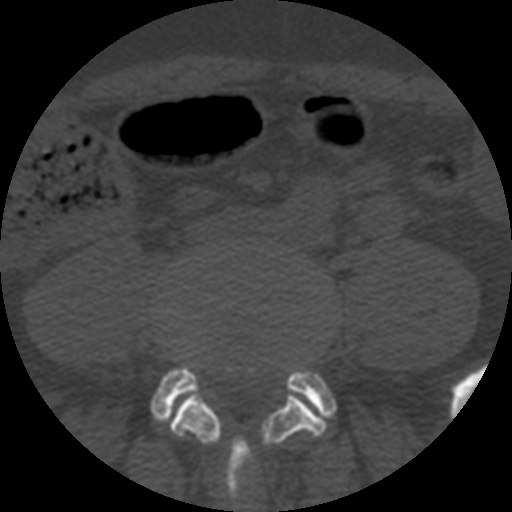
CT including the spine, one axial slice. Position 78 of 508 along the scan axis. Reconstruction kernel STANDARD. Bone window (W 1800 / L 400 HU). 1.25 mm slice thickness. 512 × 512 image matrix. Patient age 57 years. From the clinical record (not read from this slice): primary cancer: prostate.
Annotated regions visible in this slice (semi-automatically segmented with operator editing):
- L4 vertebra: bounding box <170,389,326,509> (left, top, right, bottom; pixels)
- L5 vertebra: <152,365,335,424>